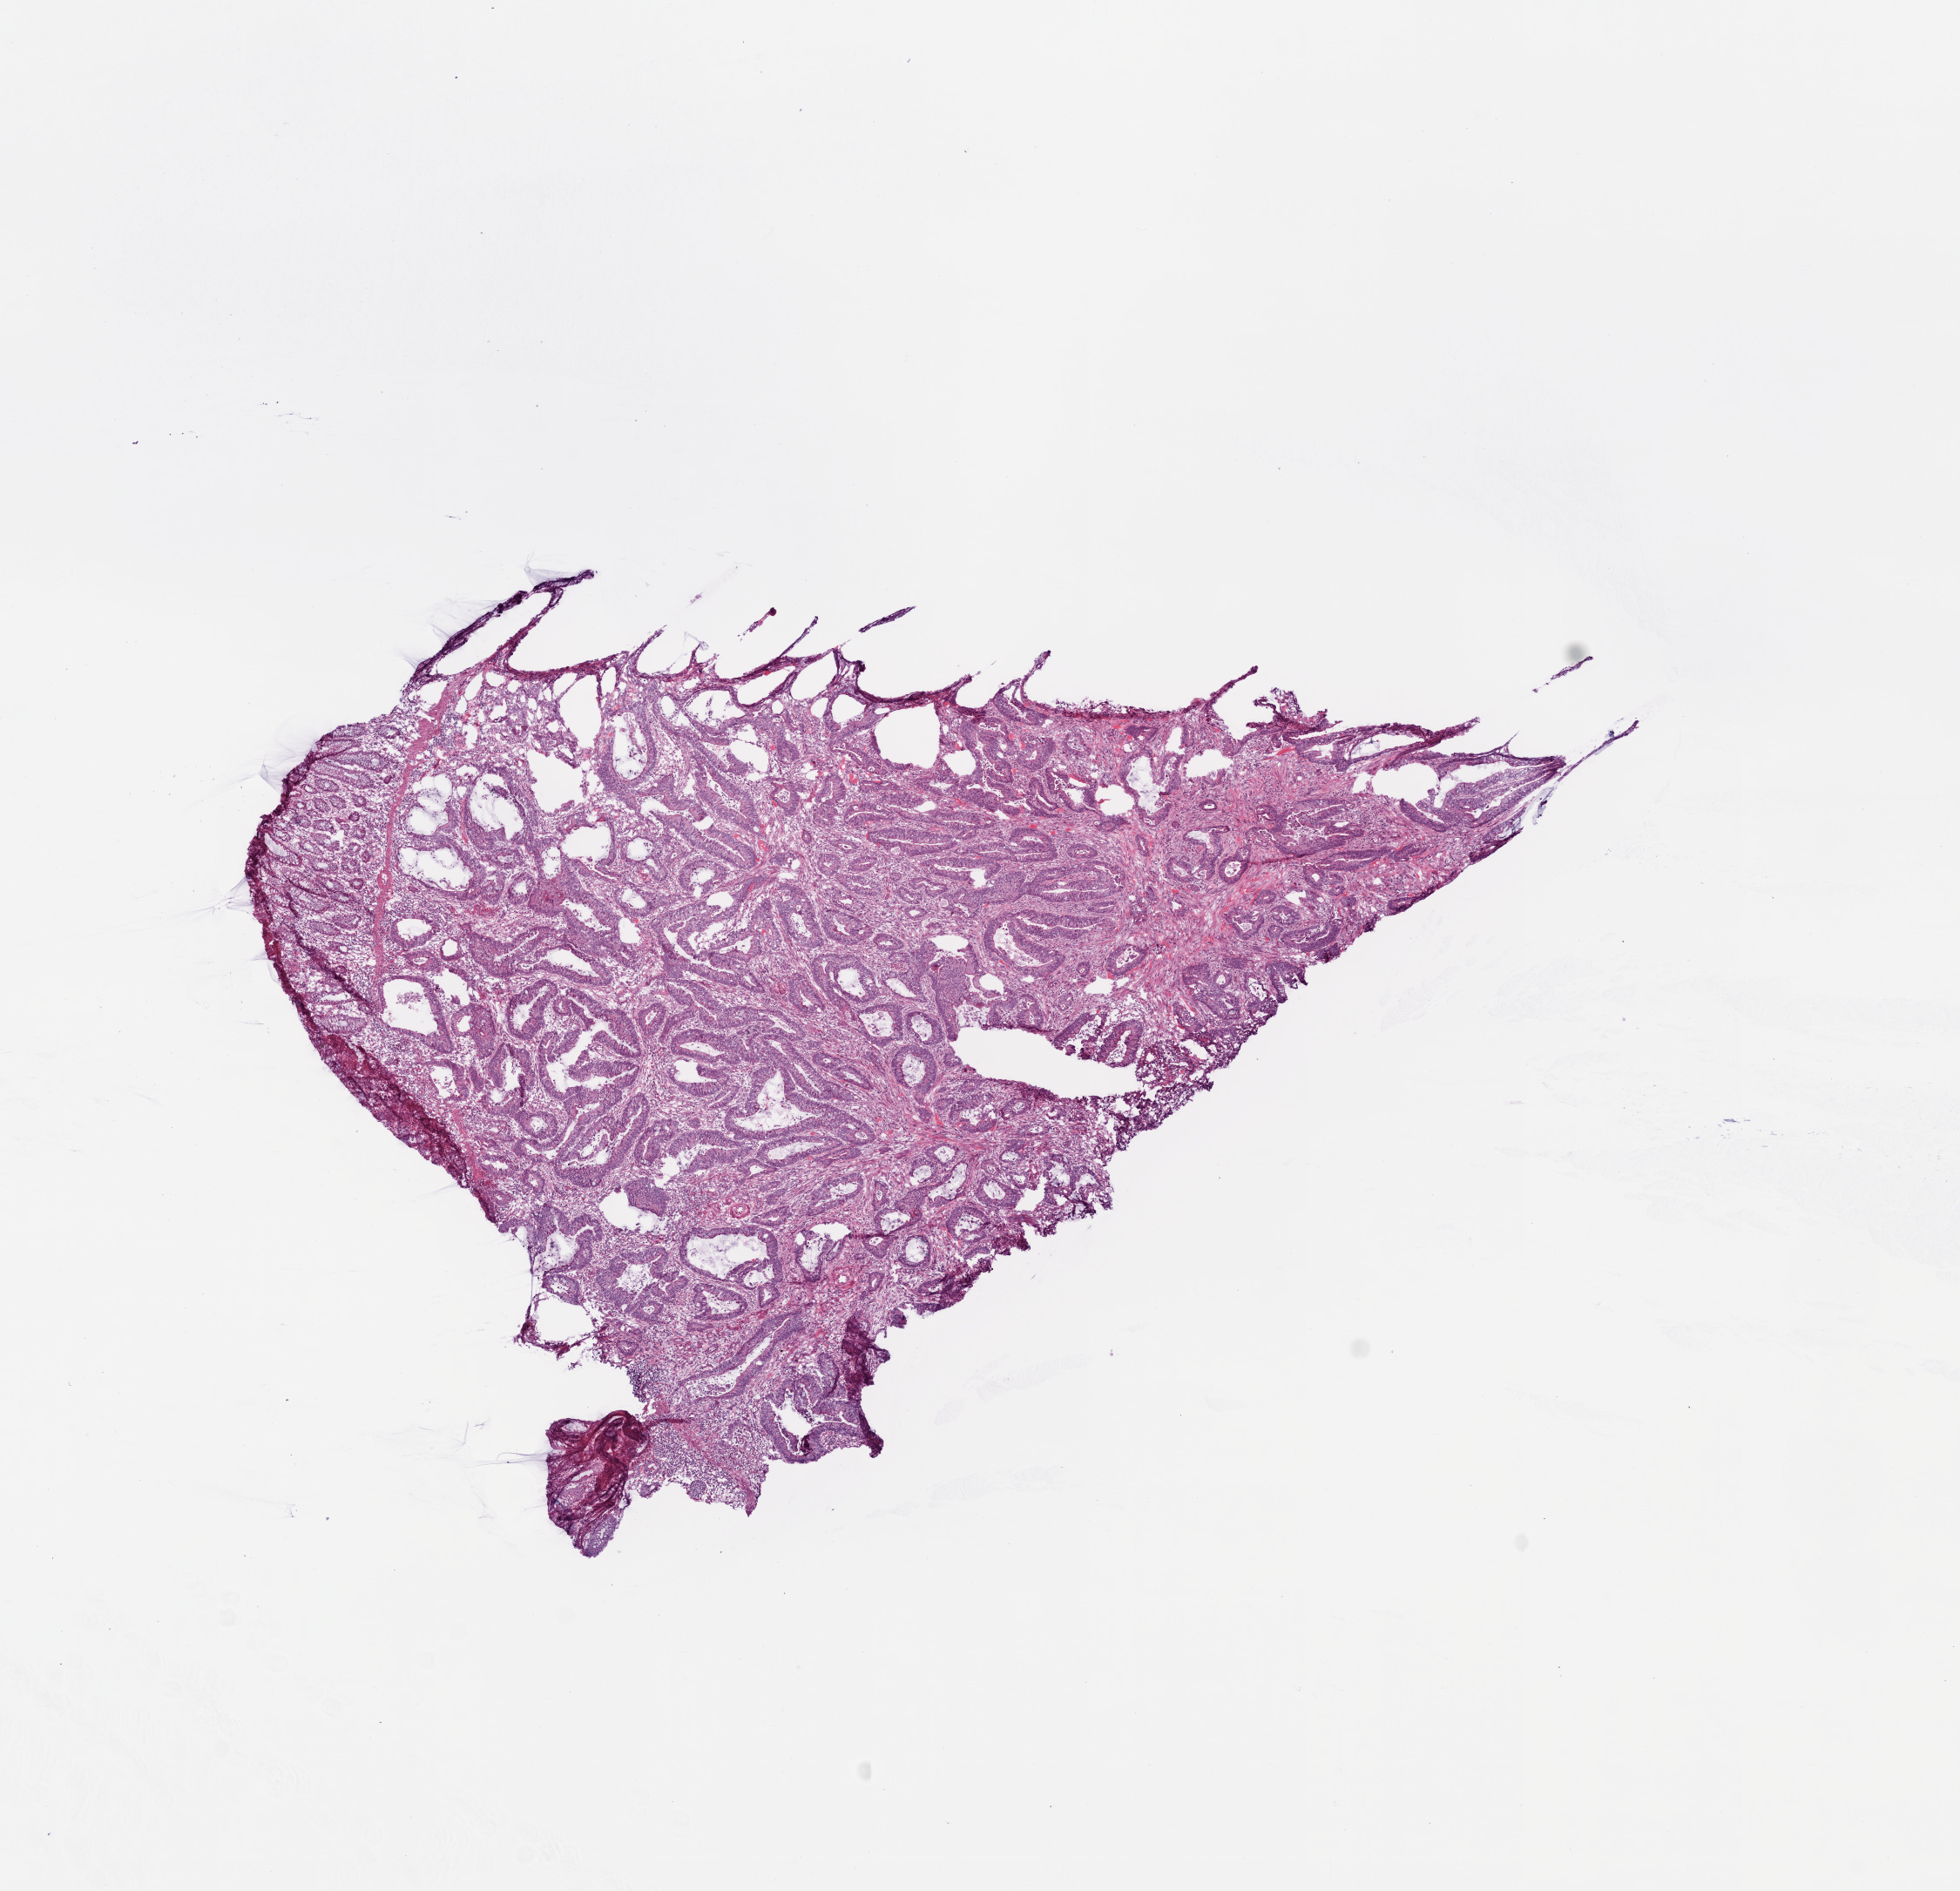
Digitized Hematoxylin and eosin (H&E) stained tissue section (whole slide) — whole scanned area (about 9.0 x 8.7 mm, from a 20x scan) shown as a low-resolution overview; frozen section from the top of the tissue portion; primary tumour sample from the colon. Male, age 74 years at initial diagnosis. Composition of this section per pathologist review: tumour cells 84%, tumour nuclei 85%, normal cells 5%, stromal cells 10%, necrosis 1%.
• AJCC pathologic stage: IIA (6th edition)
• histologic diagnosis: Adenocarcinoma, NOS
• lymph nodes positive (case pathology): 0 of 14 examined